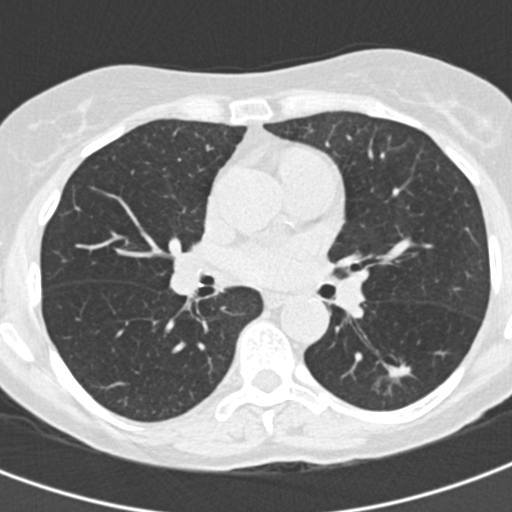
Low-dose screening chest CT, one axial slice; position 84 of 155 along the scan axis; reconstruction kernel B30f; 120 kVp; lung window (W 1500 / L -600 HU); 2 mm slice thickness; 512 × 512 image matrix.
Outlined on this slice (outlined manually by an expert reader):
- lesion 1 (tumor, lower lobe of left lung): bounding box <382,363,411,383> (left, top, right, bottom; pixels)